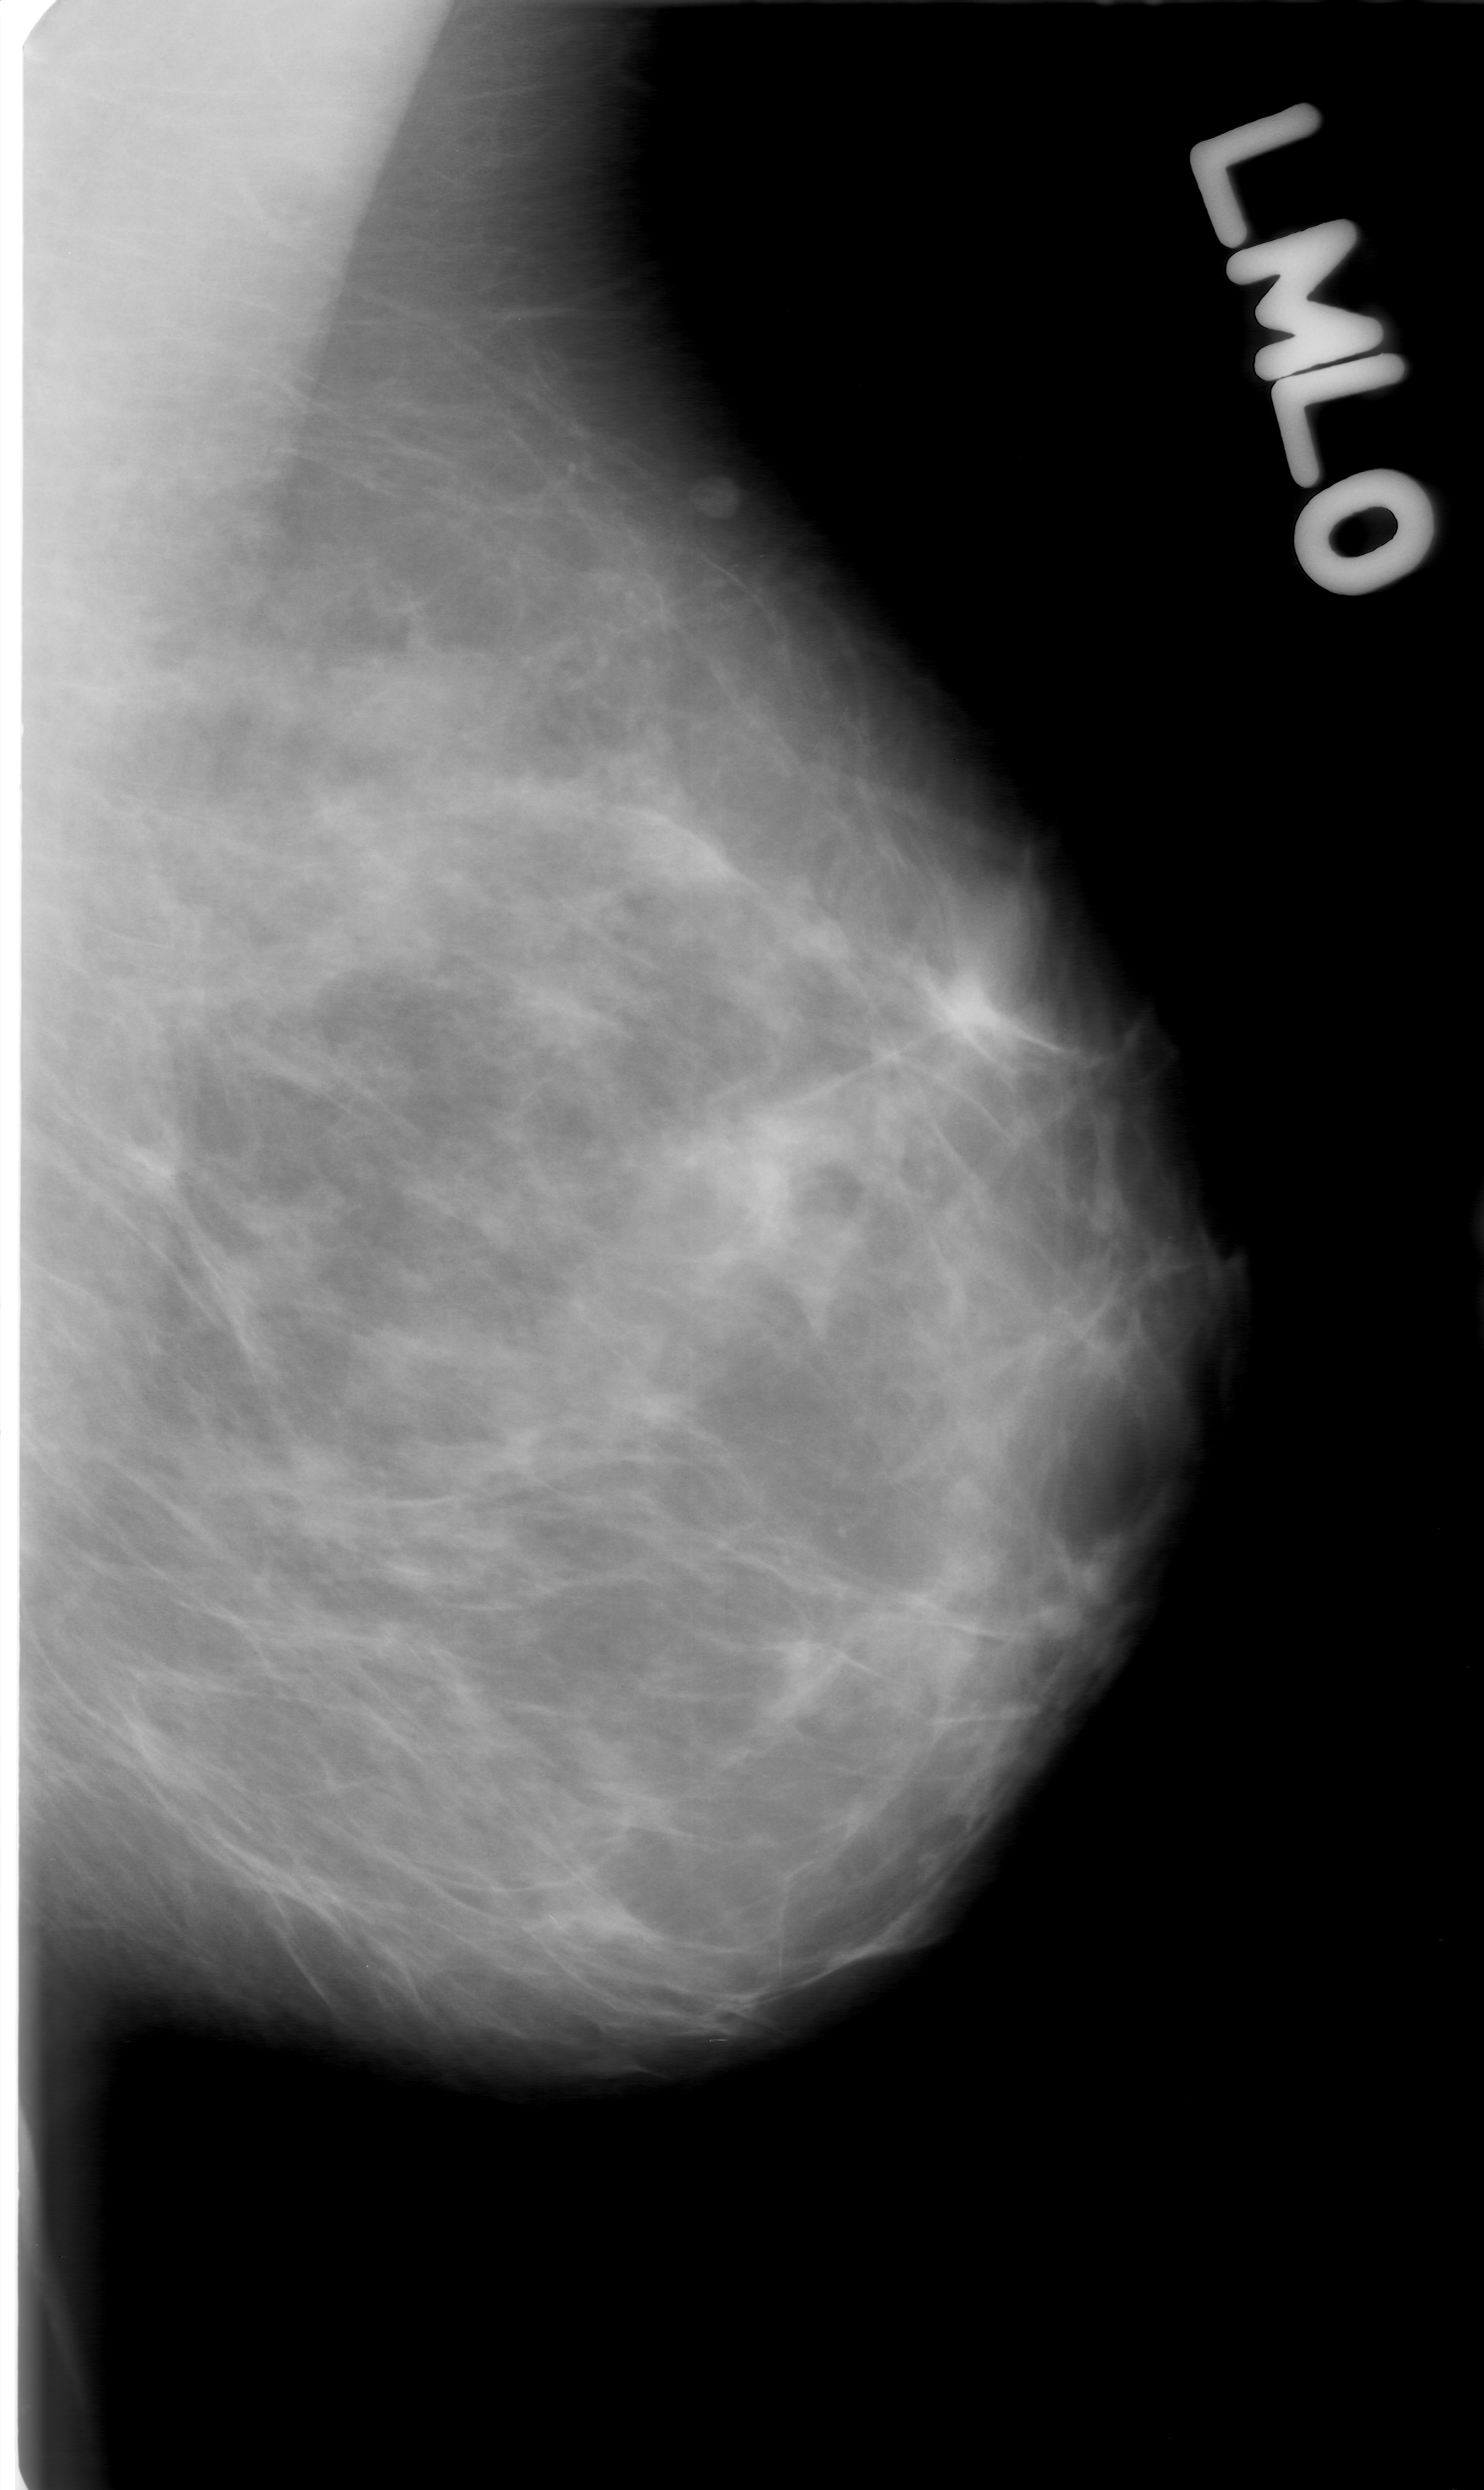
Digitized screen-film mammogram. Left breast. MLO view. BI-RADS breast density category 2 (scale 1–4). 1484 × 2490 image matrix.
Expert-marked regions of interest on this image (one box per marked abnormality):
- mass, shape oval, margins obscured; BI-RADS assessment category 0 (incomplete: needs additional imaging); pathology (as recorded): benign: bounding box (x1, y1, x2, y2) in pixels: (876, 874, 1051, 1059)